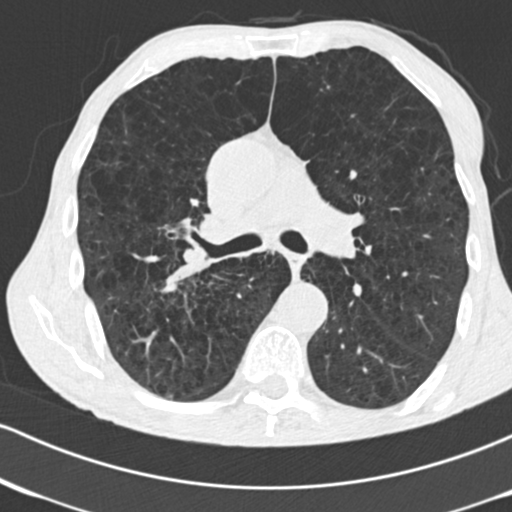
Low-dose screening chest CT, one axial slice; slice 104 of 182 in the series (ordered by position); reconstruction kernel B30f; 120 kVp; lung window (W 1500 / L -600 HU); 512 × 512 image matrix, field of view 316 × 316 mm.
Structures marked on this image (outlined manually by an expert reader):
- lesion 1 (tumor, lower lobe of right lung): box from (x=159, y=262) to (x=202, y=294) px